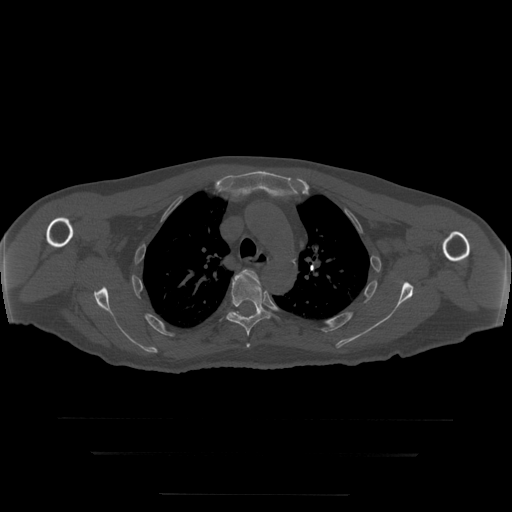
CT including the spine, one axial slice; slice 226 of 397 in the series (ordered by position); reconstruction kernel STANDARD; 120 kVp; bone window (W 1800 / L 400 HU); 1.25 mm slice thickness; 512 × 512 image matrix. Patient age 73 years. Case-level facts recorded for this patient, not image findings: primary cancer: prostate.
Annotated regions visible in this slice (semi-automatic segmentation, software-assisted and operator-edited):
- T4 vertebra: bounding box (x1, y1, x2, y2) in pixels: (239, 269, 260, 347)
- T5 vertebra: (226, 274, 271, 348)
- T6 vertebra: (231, 311, 241, 317)